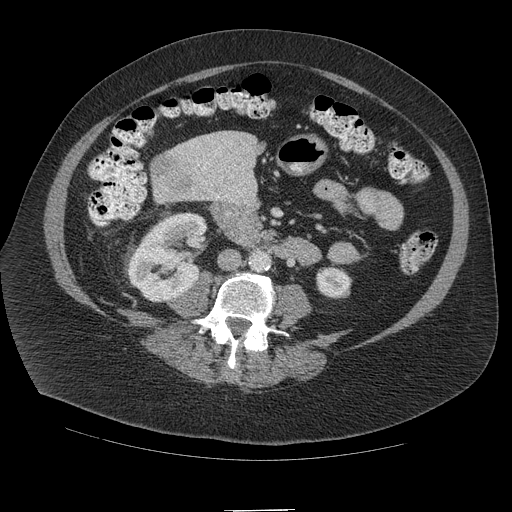
Contrast-enhanced abdominal CT (liver protocol), one axial slice. Slice 26 of 109 in the series (ordered by position). Reconstruction kernel STANDARD. Soft-tissue window (W 400 / L 40 HU). 512 × 512 image matrix, field of view 420 × 420 mm. Case-level facts recorded for this patient, not image findings: diagnosis: hepatocellular carcinoma (patient treated with transarterial chemoembolisation; whether this scan precedes or follows treatment is not stated here); TNM stage (as recorded): Stage-IVB; Child-Pugh class: A.
Outlined on this slice (semi-automatically segmented with operator editing):
- liver parenchyma outside the tumour (the mass and vessels are separate outlines, so this box may not span the whole liver): box from (x=200, y=130) to (x=260, y=172) px
- mass: (x=151, y=155)–(x=184, y=184)
- liver vessels: (x=214, y=147)–(x=221, y=155)